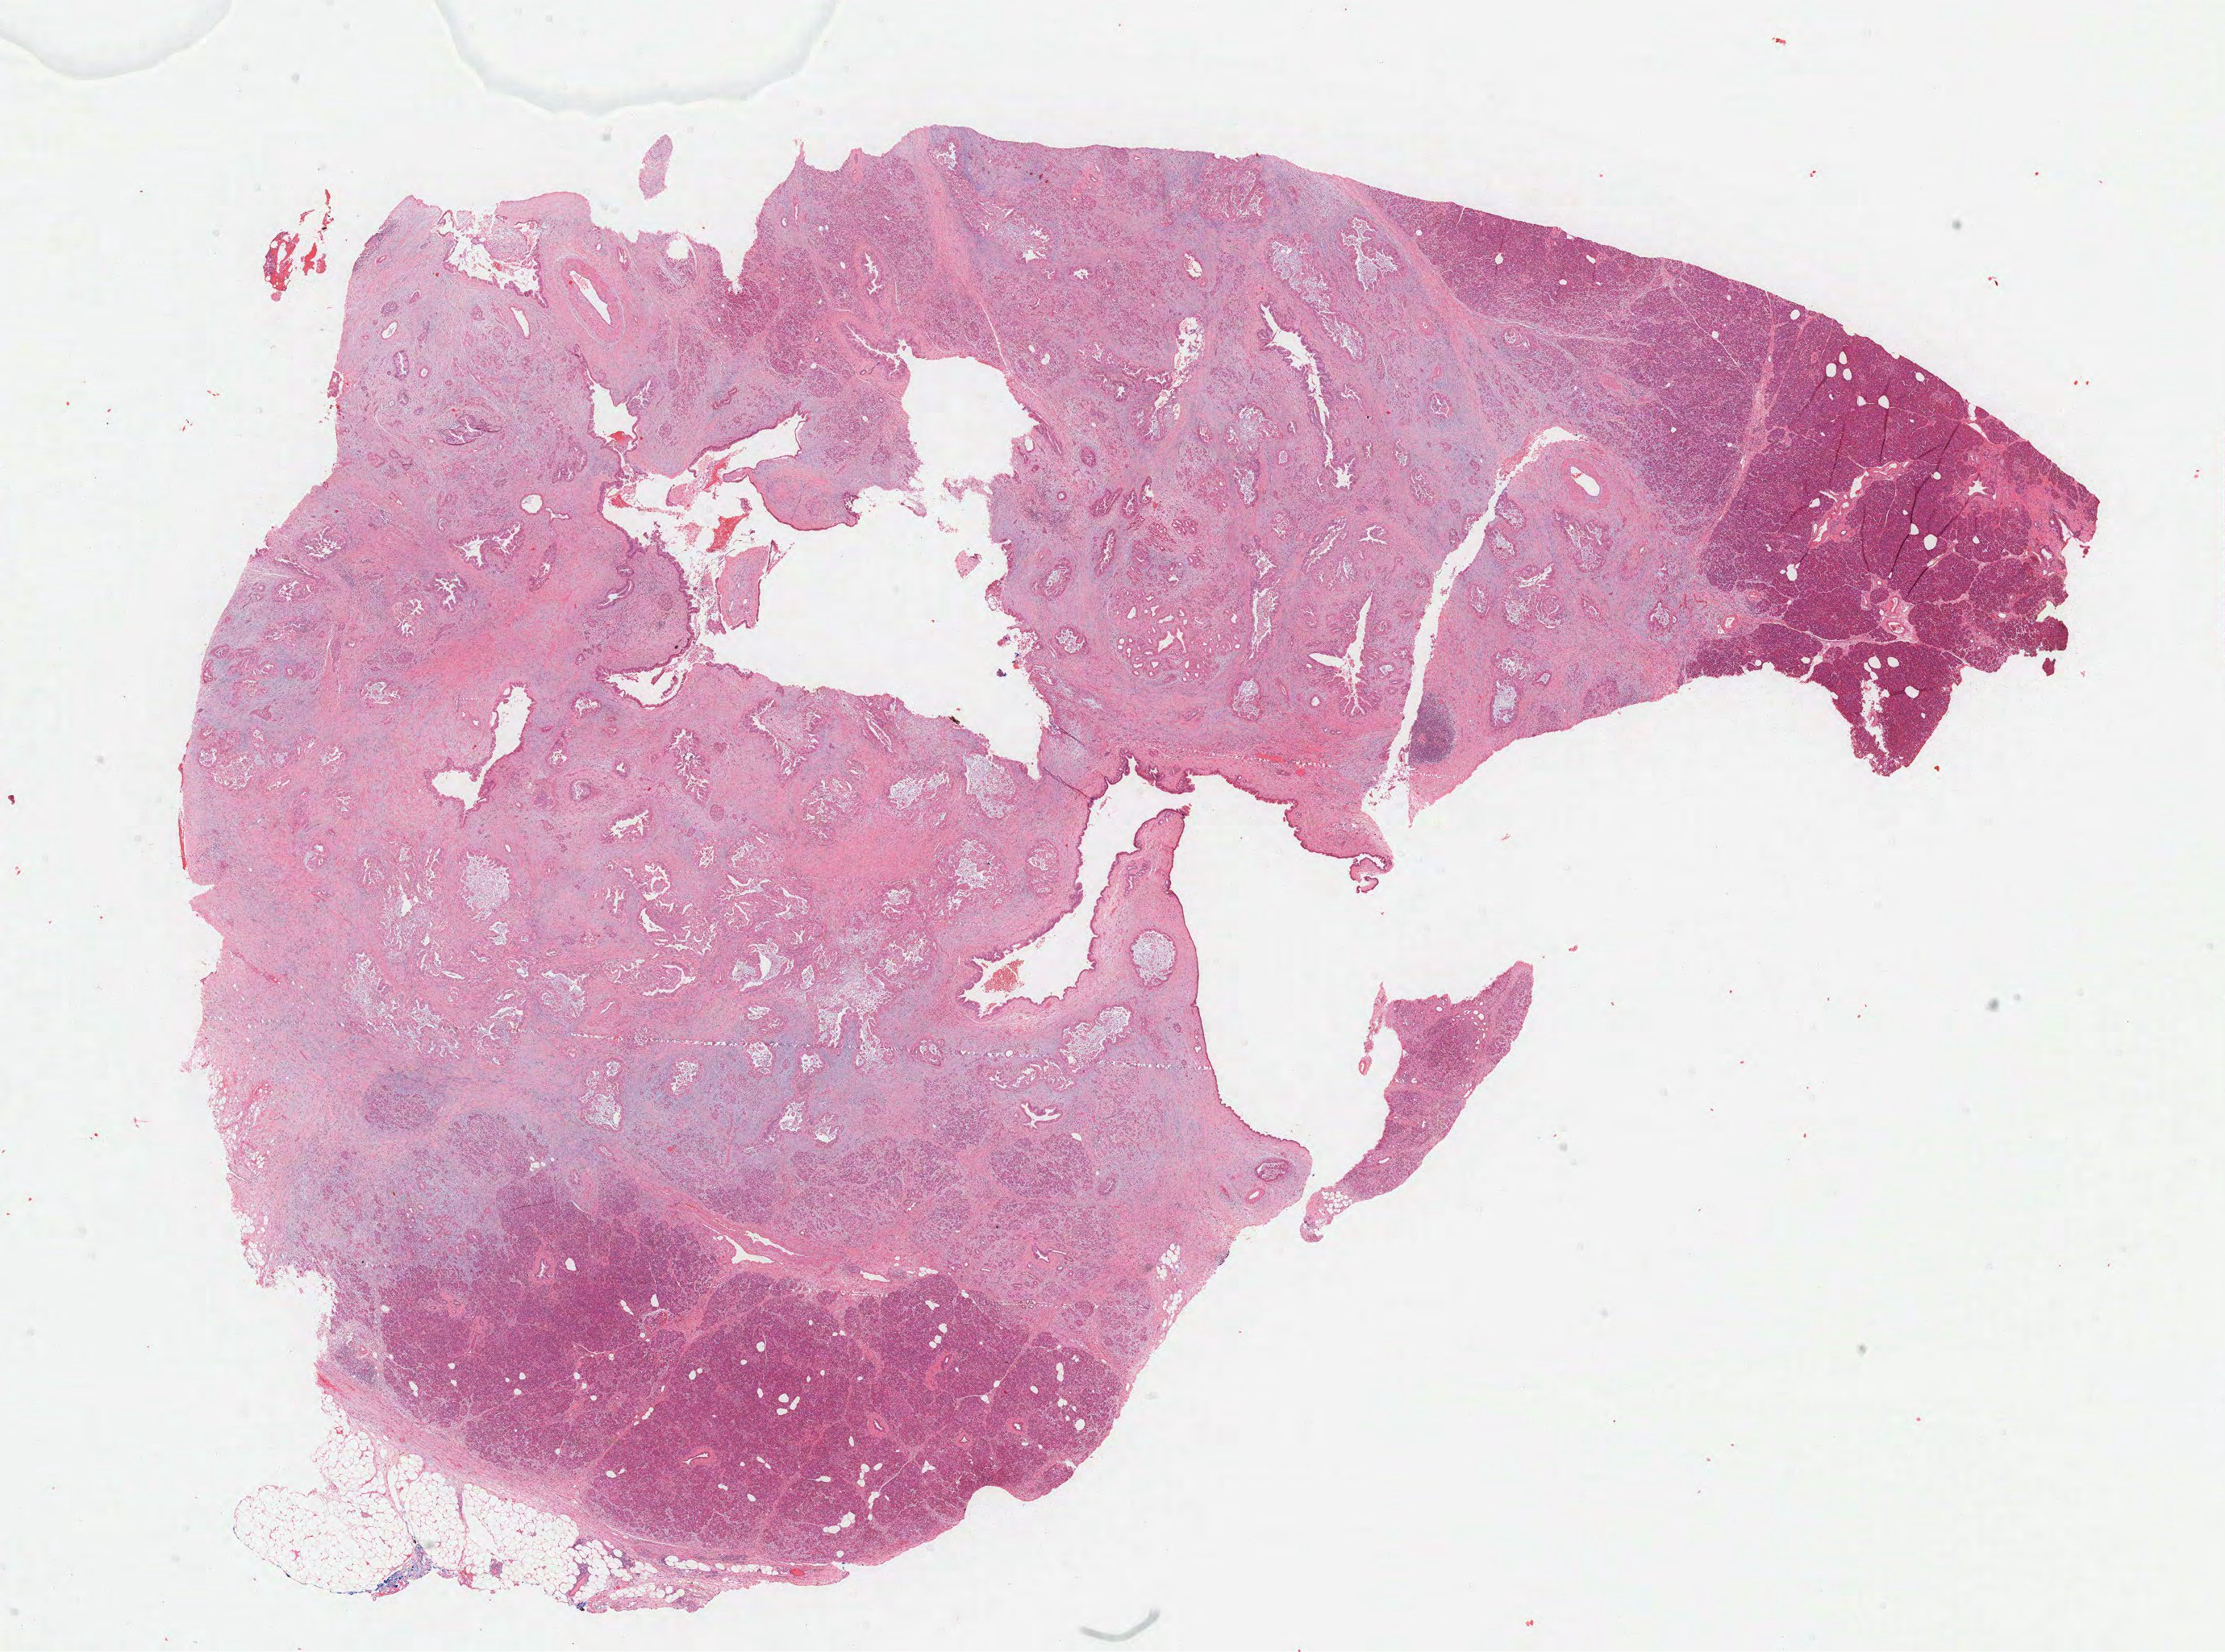
Whole-slide histology image, H&E-stained — whole scanned area (about 22.3 x 16.6 mm, slide scanned at 40x) shown as a low-resolution overview, FFPE section, primary tumour sample from the pancreas. Female, age 66 years at initial diagnosis.
Diagnosis: Infiltrating duct carcinoma, NOS (body of pancreas).